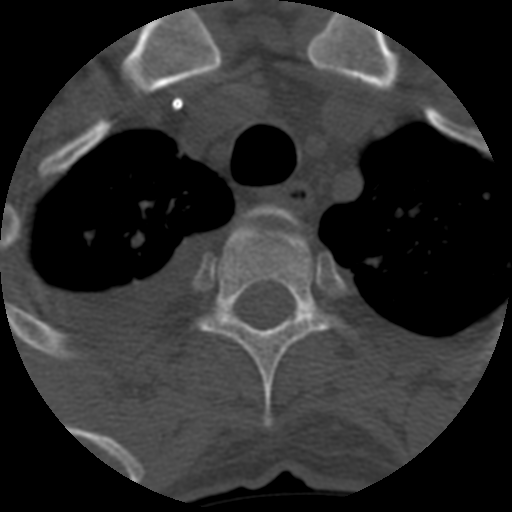
CT including the spine, one axial slice; slice 489 of 708 in the series (ordered by position); reconstruction kernel STANDARD; 120 kVp; one of 3 acquisitions stored at this slice position; bone window (W 1800 / L 400 HU); 1.25 mm slice thickness; 512 × 512 image matrix. Patient age 55 years. From the clinical record (not read from this slice): primary cancer: colon; vertebrae with lytic lesions (as recorded): T12, L1, L5.
Outlined on this slice (semi-automatic segmentation, software-assisted and operator-edited):
- T2 vertebra: bounding box <245,206,285,220> (left, top, right, bottom; pixels)
- T3 vertebra: <200,216,328,428>
- T4 vertebra: <292,311,302,321>